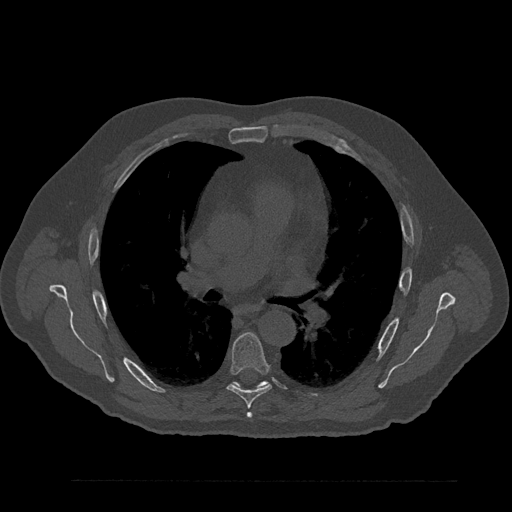
CT including the spine, one axial slice; position 548 of 797 along the scan axis; 120 kVp; bone window (W 1800 / L 400 HU); 0.5 mm slice thickness; 512 × 512 image matrix, field of view 430 × 430 mm. Patient: male, 61 years. From the clinical record (not read from this slice): primary cancer: prostate.
Annotated regions visible in this slice (semi-automatically segmented with operator editing):
- T5 vertebra: box from (x=248, y=413) to (x=251, y=417) px
- T6 vertebra: (x=227, y=333)–(x=272, y=416)
- T7 vertebra: (x=236, y=381)–(x=268, y=387)